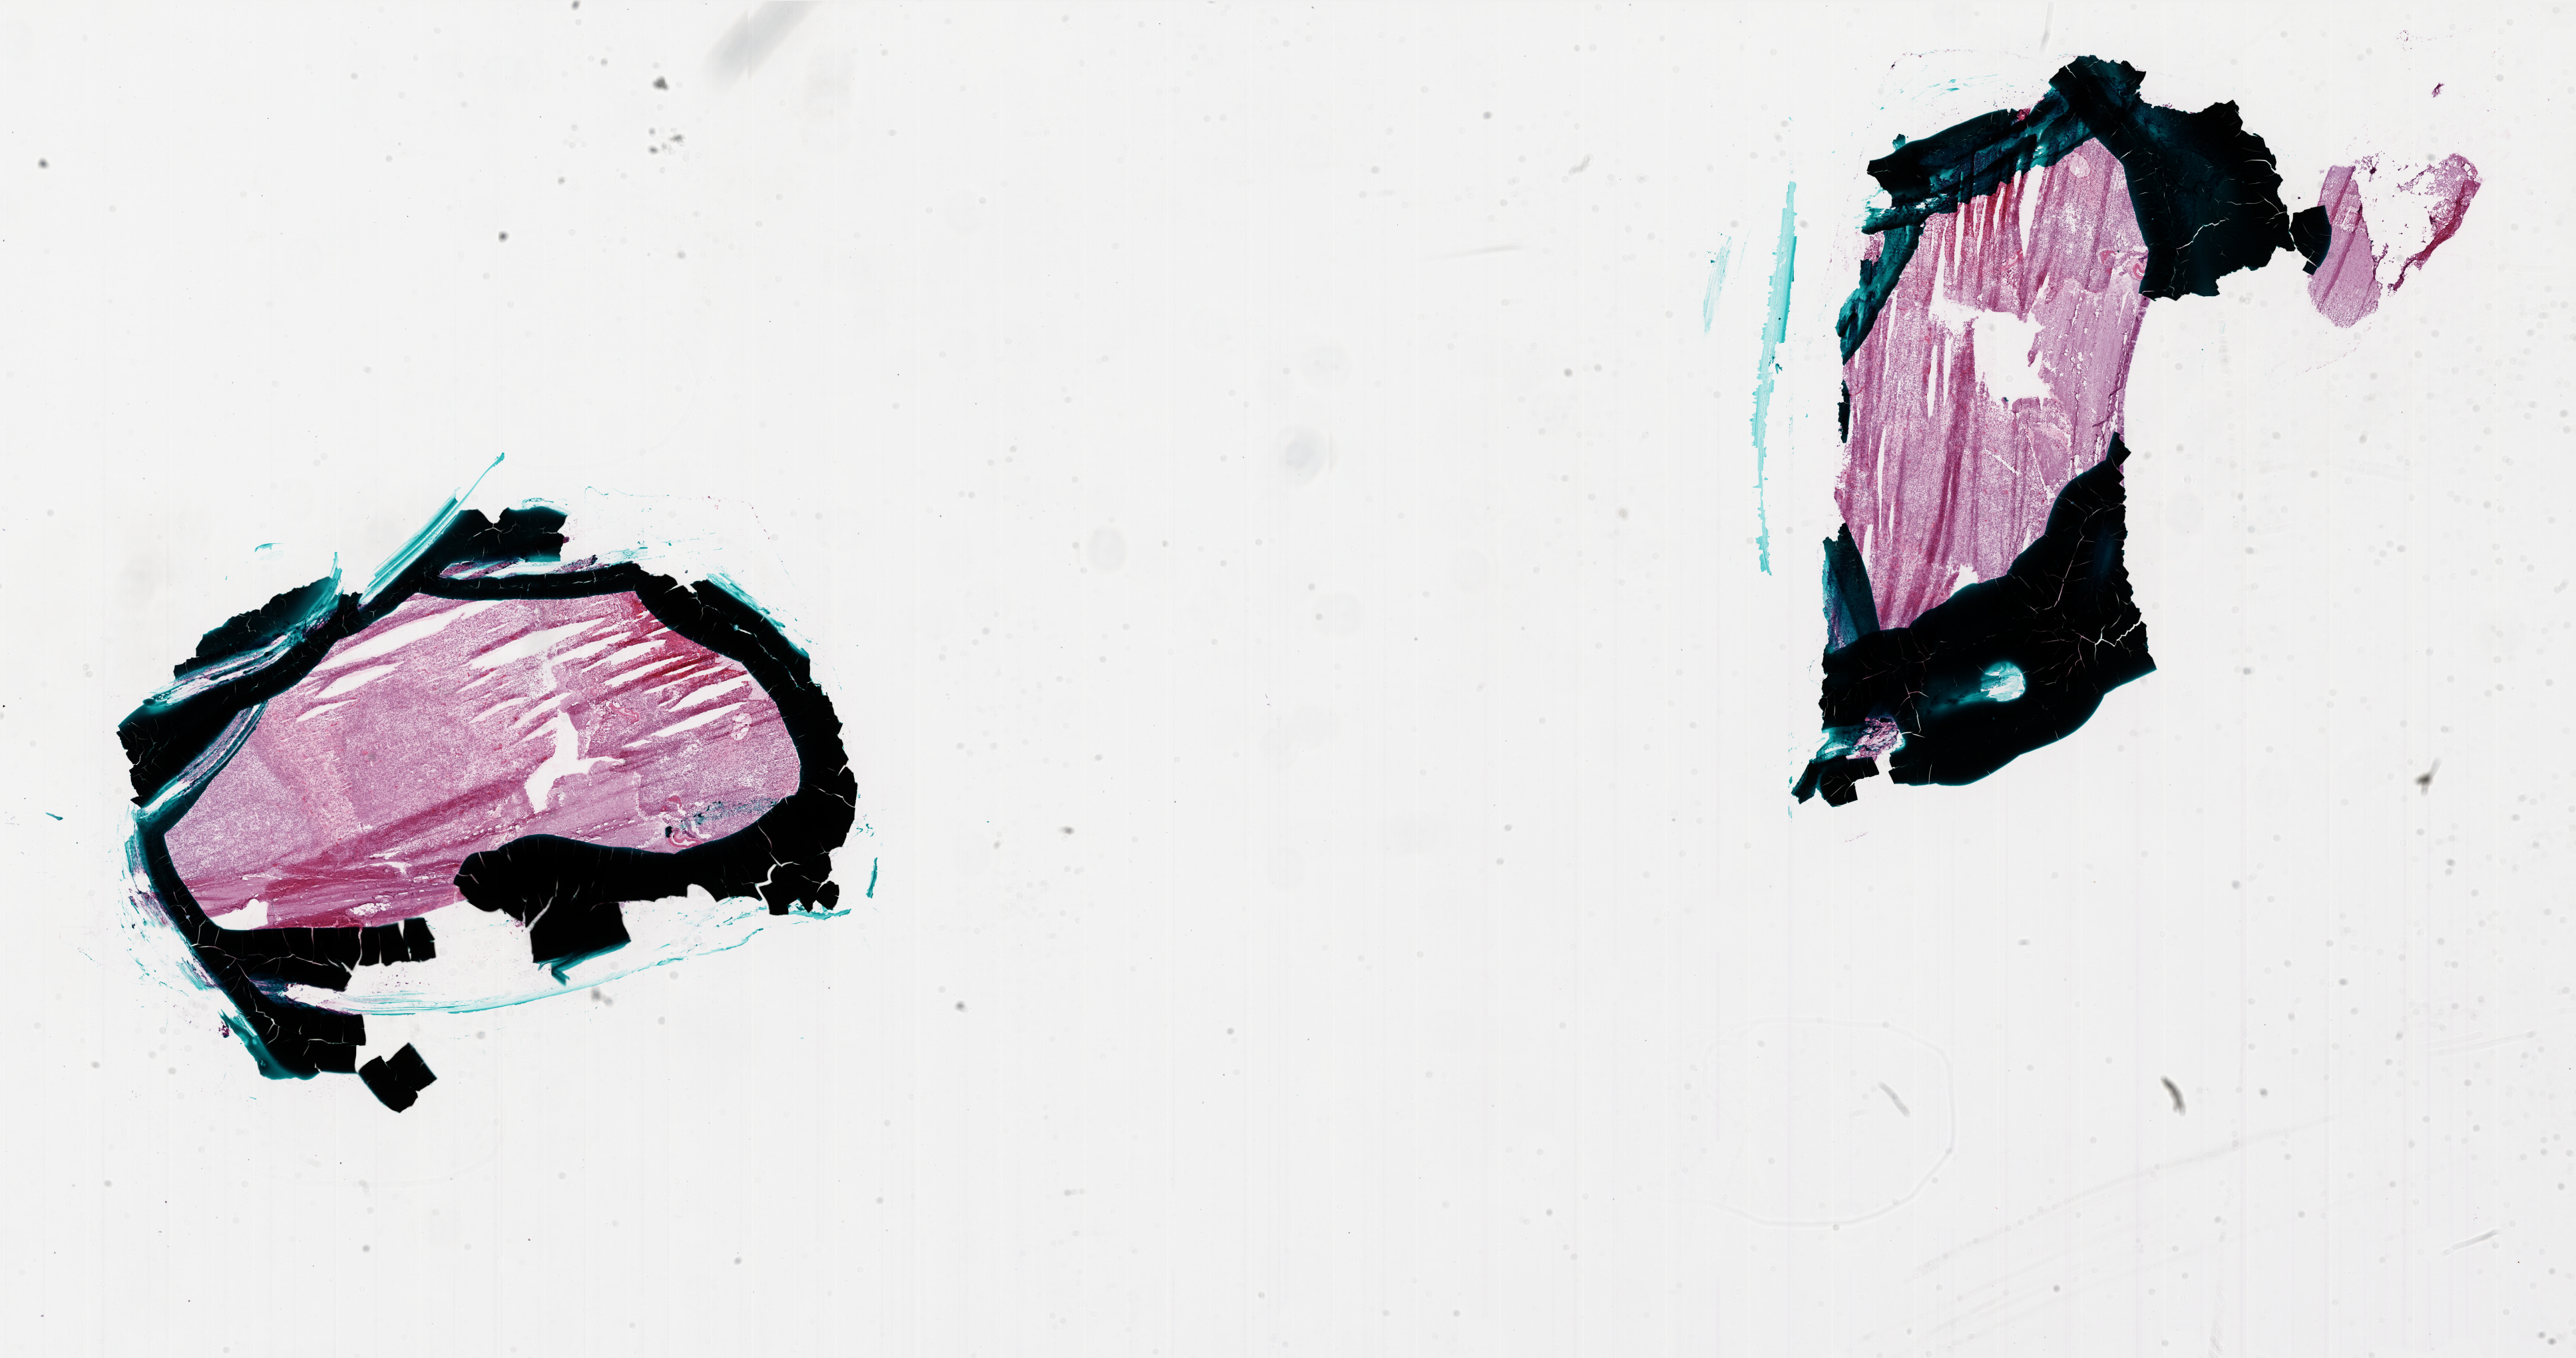
Digitized H&E-stained tissue section (whole slide), shown as a low-resolution overview of the whole scanned area (about 31.0 x 16.3 mm, from a 20x scan), frozen section, sample: primary tumour, brain. Patient: male, age at initial diagnosis 64 years. Pathologist review of this section (percent, as recorded): tumour cells 65%, tumour nuclei 80%, normal cells 25%, stromal cells 0%, necrosis 10%.
Pathologic diagnosis: Glioblastoma.